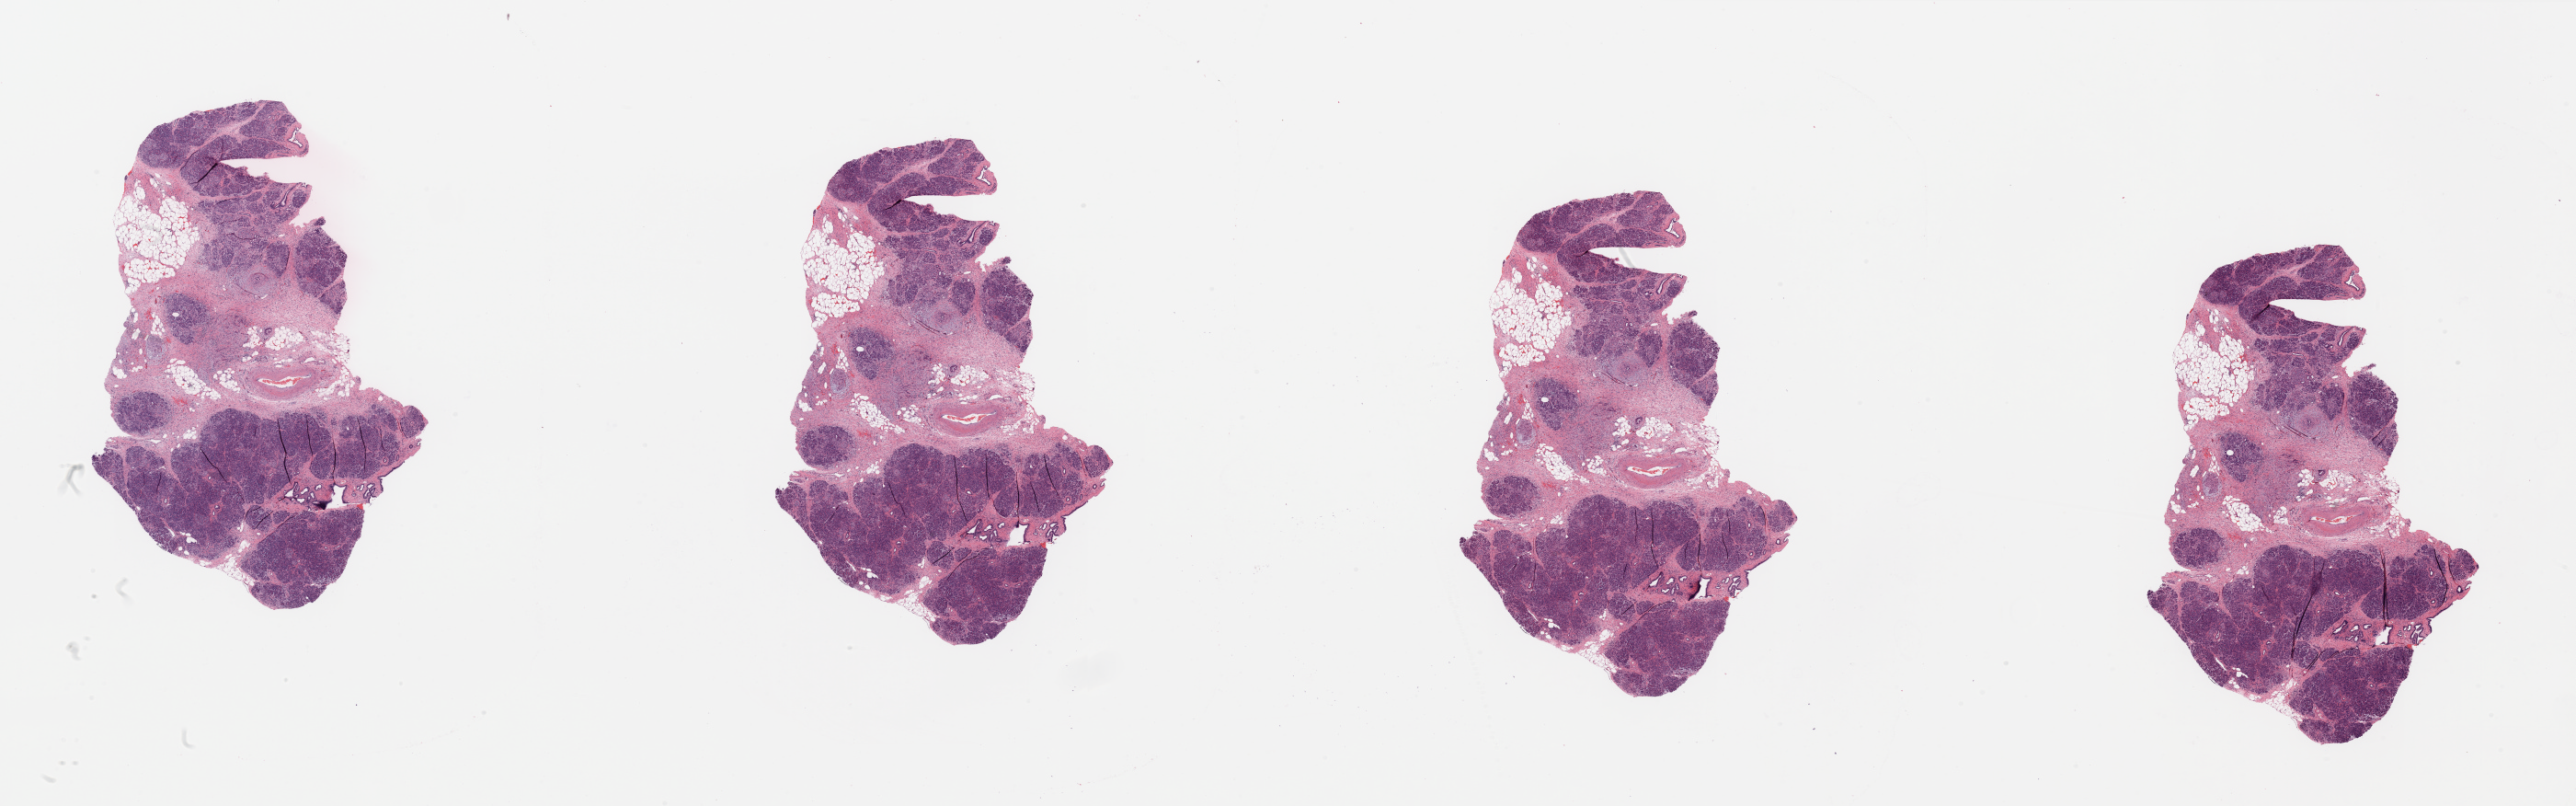
Whole-slide histology image, H&E-stained — whole scanned area (about 44.3 x 13.9 mm) shown as a low-resolution overview. Normal (non-tumour) tissue sample, sampled site: pancreas. 80-year-old male patient.
This section: normal (non-tumour) tissue from the same patient. Patient diagnosis: Infiltrating duct carcinoma, NOS.